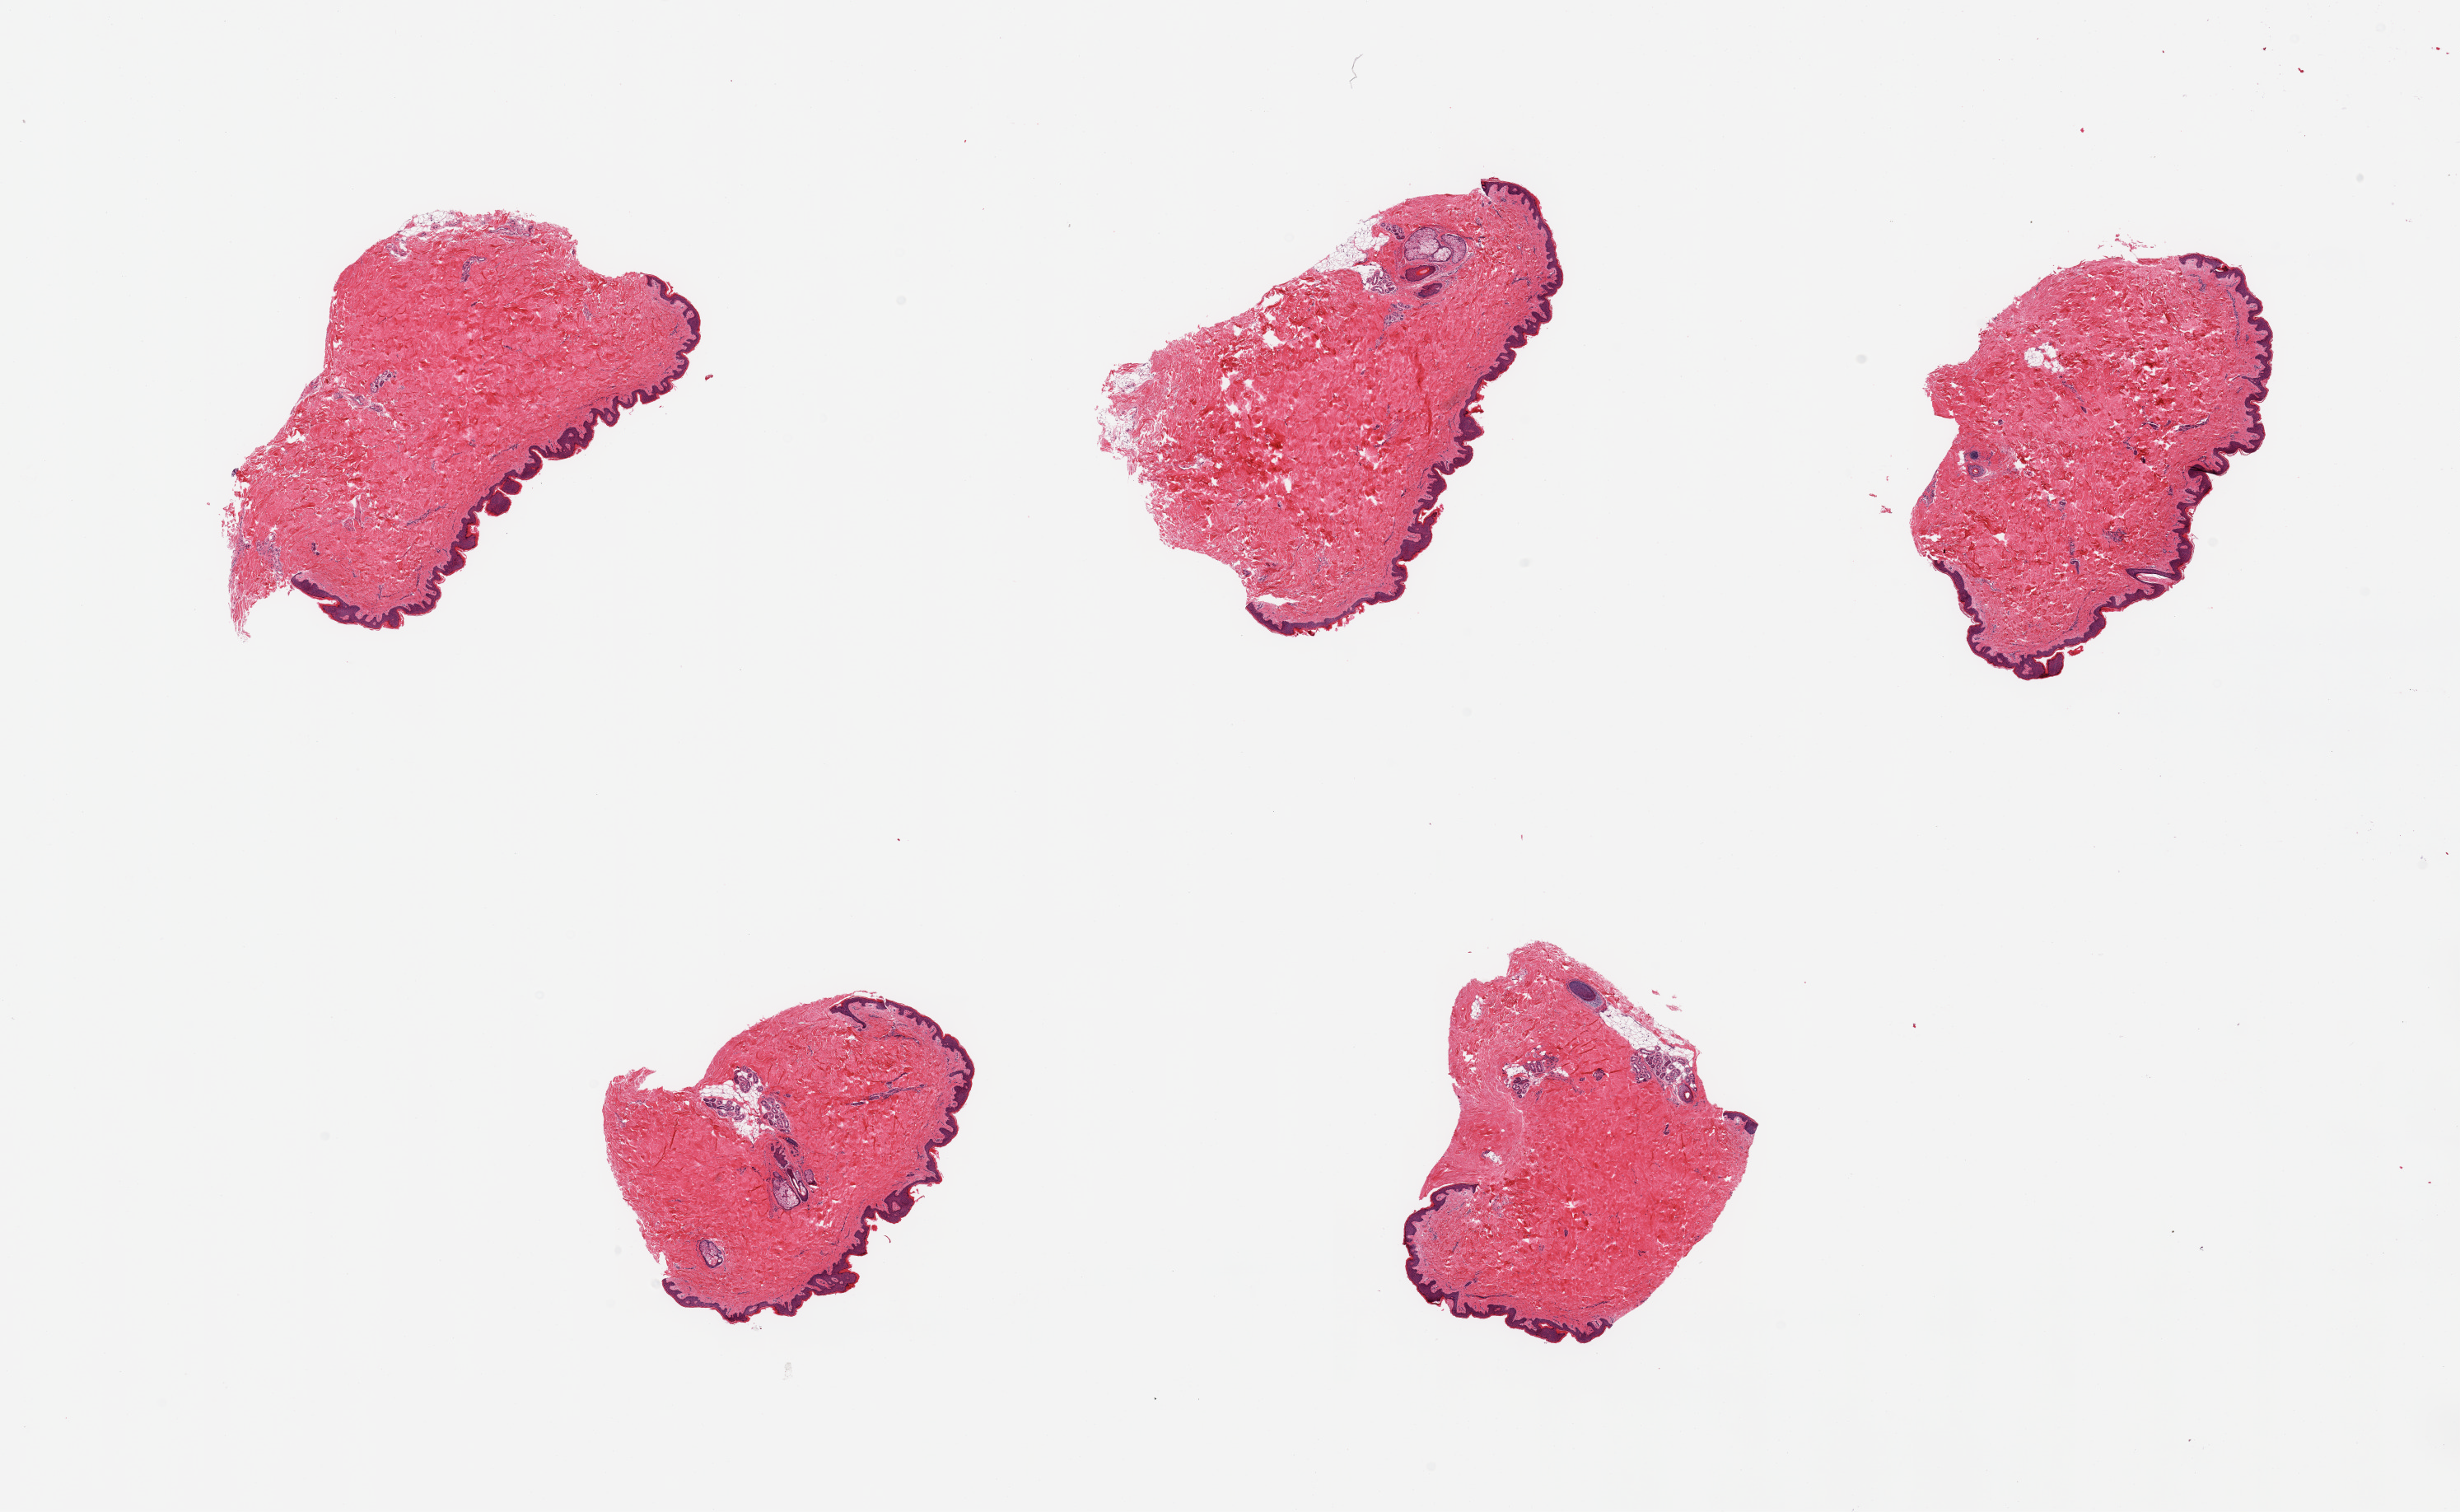
Whole-slide image, hematoxylin and eosin (H&E) stain, brightfield, a low-resolution overview of the entire scanned area, about 23.6 x 14.5 mm (slide scanned at 20x). PAXgene-fixed, paraffin-embedded tissue. Target tissue: skin of suprapubic region. Donor tissue sample. Donor sex: male.
• reviewer comment on this tissue sample: 5 pieces; well trimmed, scant internal fat